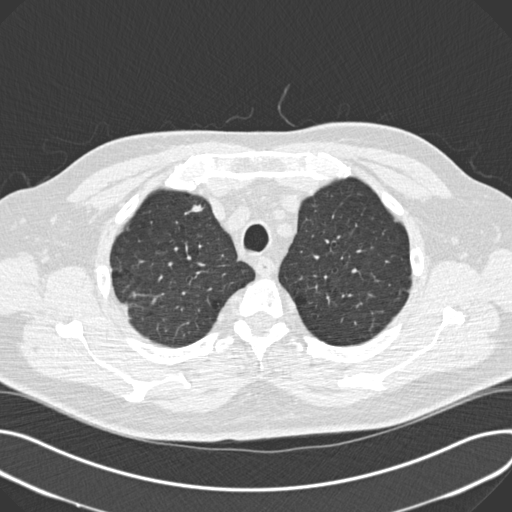
Low-dose screening chest CT, one axial slice; position 150 of 180 along the scan axis; reconstruction kernel B30f; lung window (W 1500 / L -600 HU); 512 × 512 image matrix, field of view 376 × 376 mm.
Annotated regions visible in this slice (manually delineated by an expert):
- lesion 2 (tumor, upper lobe of right lung): bounding box [x1, y1, x2, y2] px = [191, 205, 203, 212]